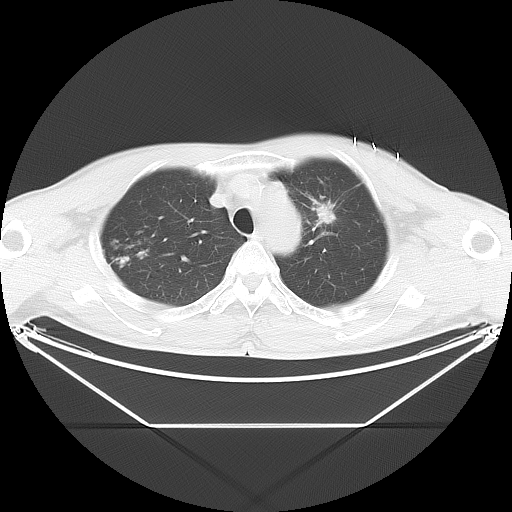
Chest CT, one axial slice; slice 22 of 28 in the series (ordered by position); reconstruction kernel LUNG; 120 kVp; lung window (W 1500 / L -600 HU); 5 mm slice thickness; 512 × 512 image matrix, field of view 443 × 443 mm. Patient: male, 60 years. Case-level facts recorded for this patient, not image findings: clinical TNM (as recorded): T2 N1 M0.
Structures marked on this image (rectangle marked by the reading radiologist):
- lung tumour (recorded histology: adenocarcinoma): box from (x=310, y=199) to (x=345, y=231) px